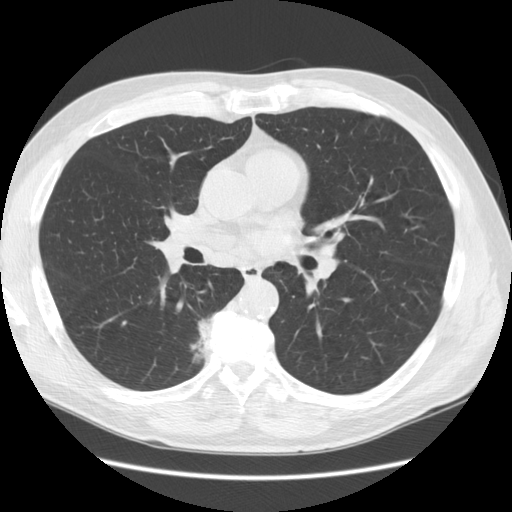
Chest CT (low-dose screening protocol), one axial image; second annual screen; lung window (W 1500 / L -600 HU); standard (soft-tissue) reconstruction kernel (STANDARD); slice 63 of 133 in the series. Male participant, aged 69 years at enrolment. Former smoker at enrolment.
Lesion marked by an expert reader, bounding box <169,306,233,368> (left, top, right, bottom; pixels). The screening reader recorded 2 non-calcified nodules or masses ≥4 mm on this exam (right lower lobe, right middle lobe); which of them this box marks is not recorded. Participant outcome: lung cancer diagnosed 88 days after this screen — bronchiolo-alveolar adenocarcinoma, NOS, right lower lobe, well differentiated (G1), stage IB (AJCC 6th edition), 23 mm at pathology.